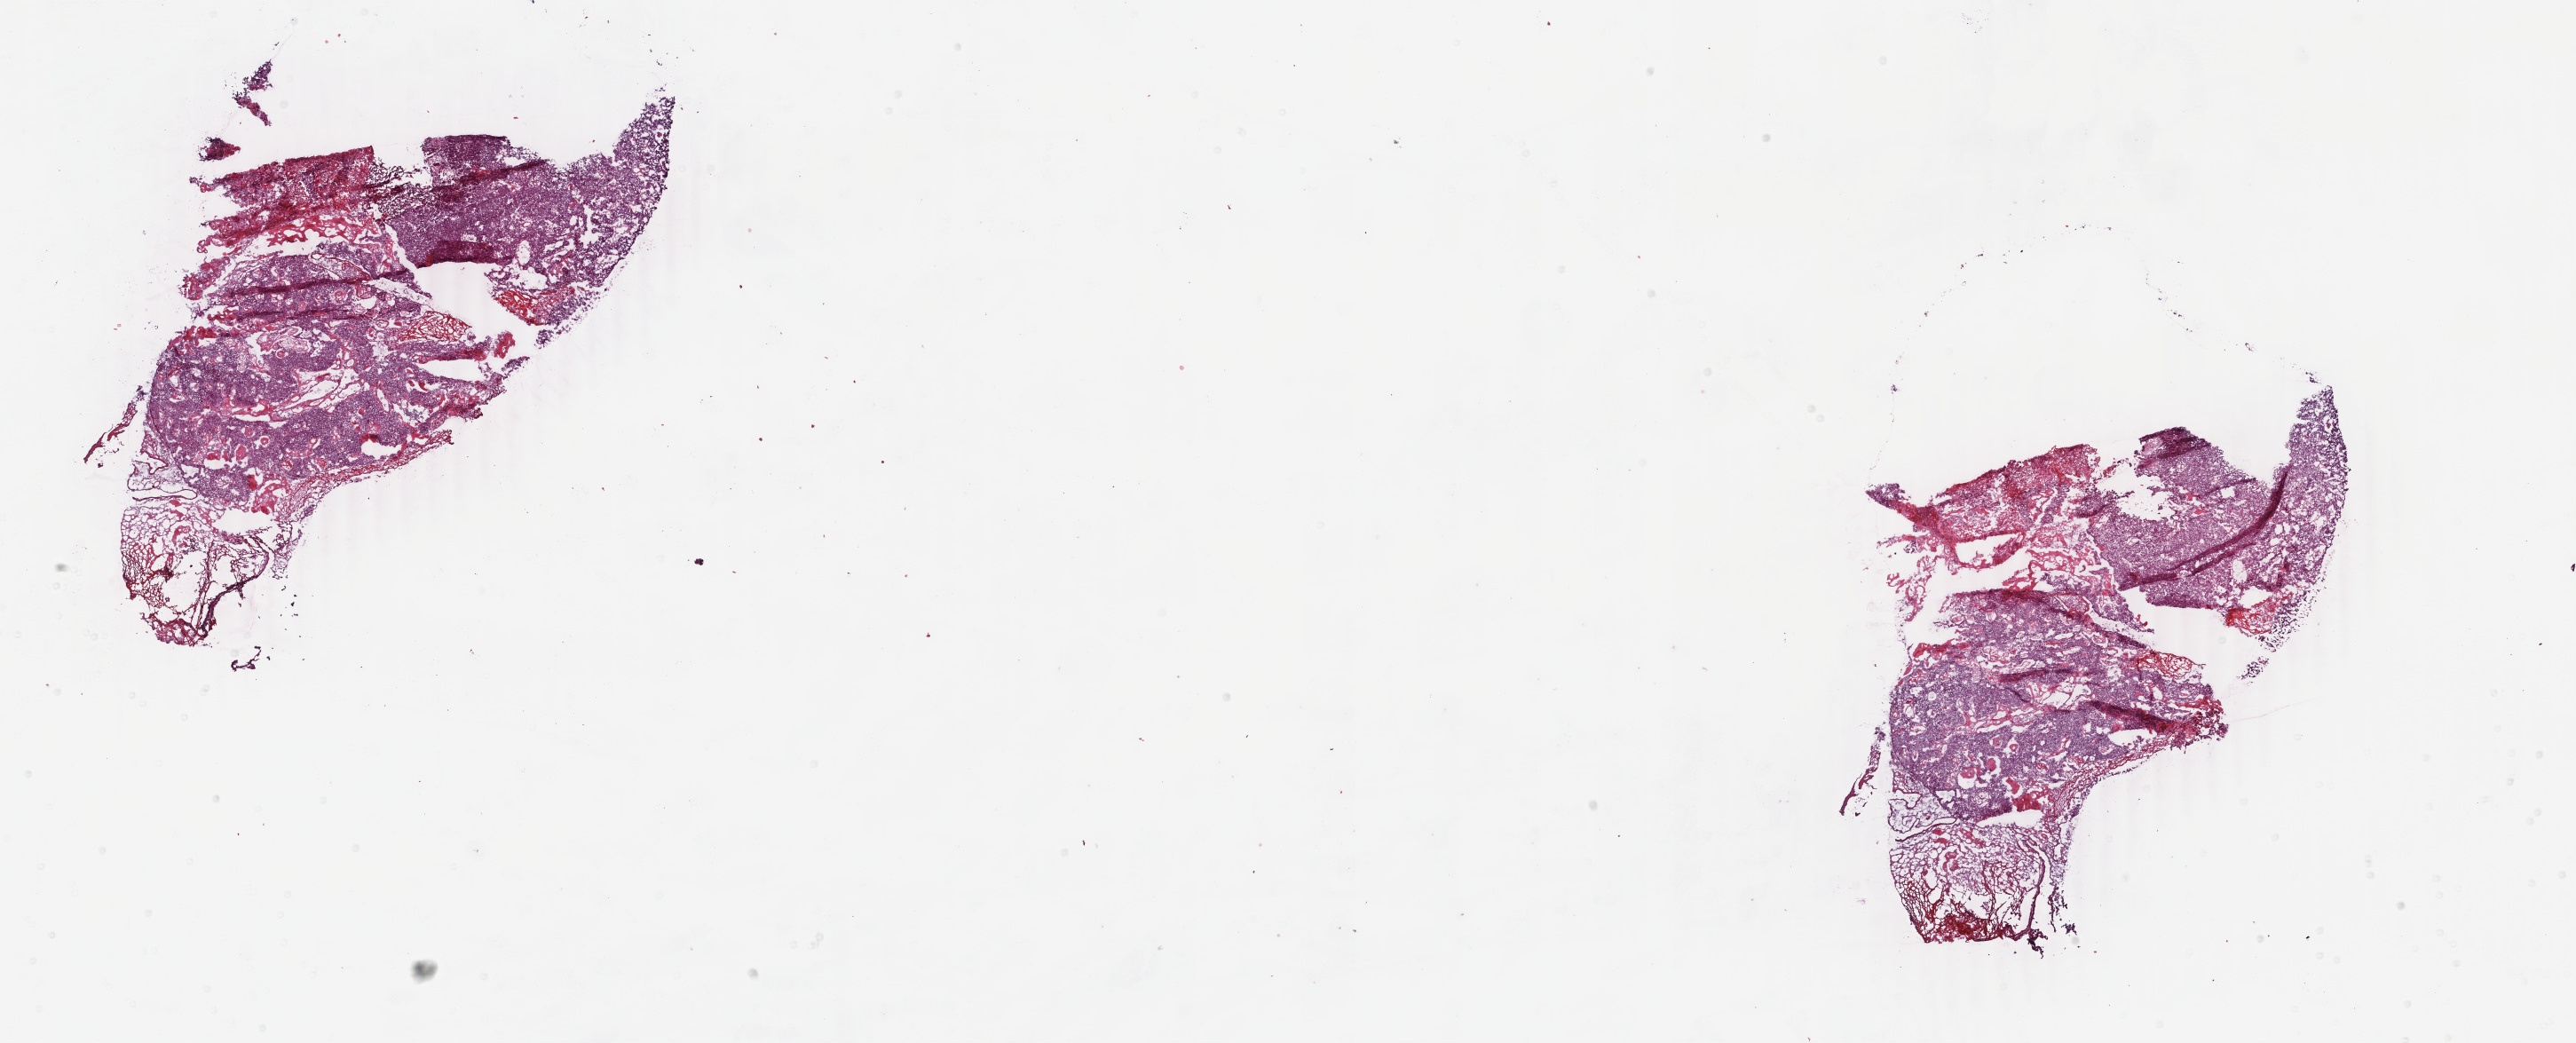
Digitized Hematoxylin and eosin (H&E) stained tissue section (whole slide), shown as a low-resolution overview of the whole scanned area (about 23.1 x 9.3 mm, from a 40x scan). Frozen section from the bottom of the tissue portion. Uterus, primary tumour sample. Patient: female, age at initial diagnosis 71 years. Histologic grade: G3 (poorly differentiated). Pathologist review of this section (percent, as recorded): tumour cells 75%, tumour nuclei 95%, normal cells 3%, stromal cells 2%, necrosis 20%. Infiltration values recorded for this section: lymphocyte infiltration 0%, monocyte infiltration 4%, neutrophil infiltration 0%.
FIGO stage: IB. Histologic diagnosis: Endometrioid adenocarcinoma, NOS (endometrium).